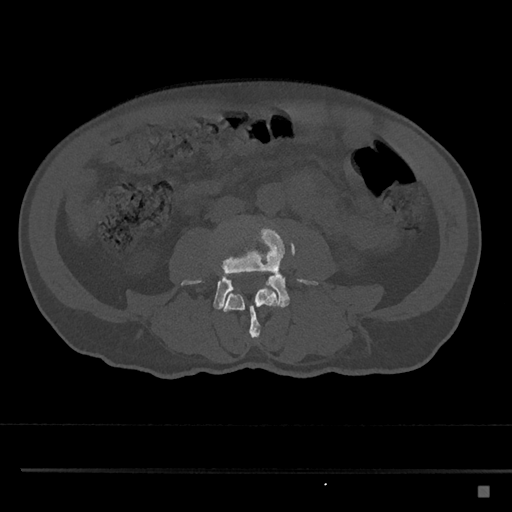
CT including the spine, one axial slice; position 663 of 797 along the scan axis; reconstruction kernel Br40s/3; bone window (W 1800 / L 400 HU); 0.5 mm slice thickness; 512 × 512 image matrix, field of view 391 × 391 mm. Male patient, age 59 years. Case-level facts recorded for this patient, not image findings: primary cancer: prostate.
Outlined on this slice (semi-automatically segmented with operator editing):
- L3 vertebra: box from (x=222, y=284) to (x=281, y=339) px
- L4 vertebra: (x=181, y=223)–(x=318, y=310)